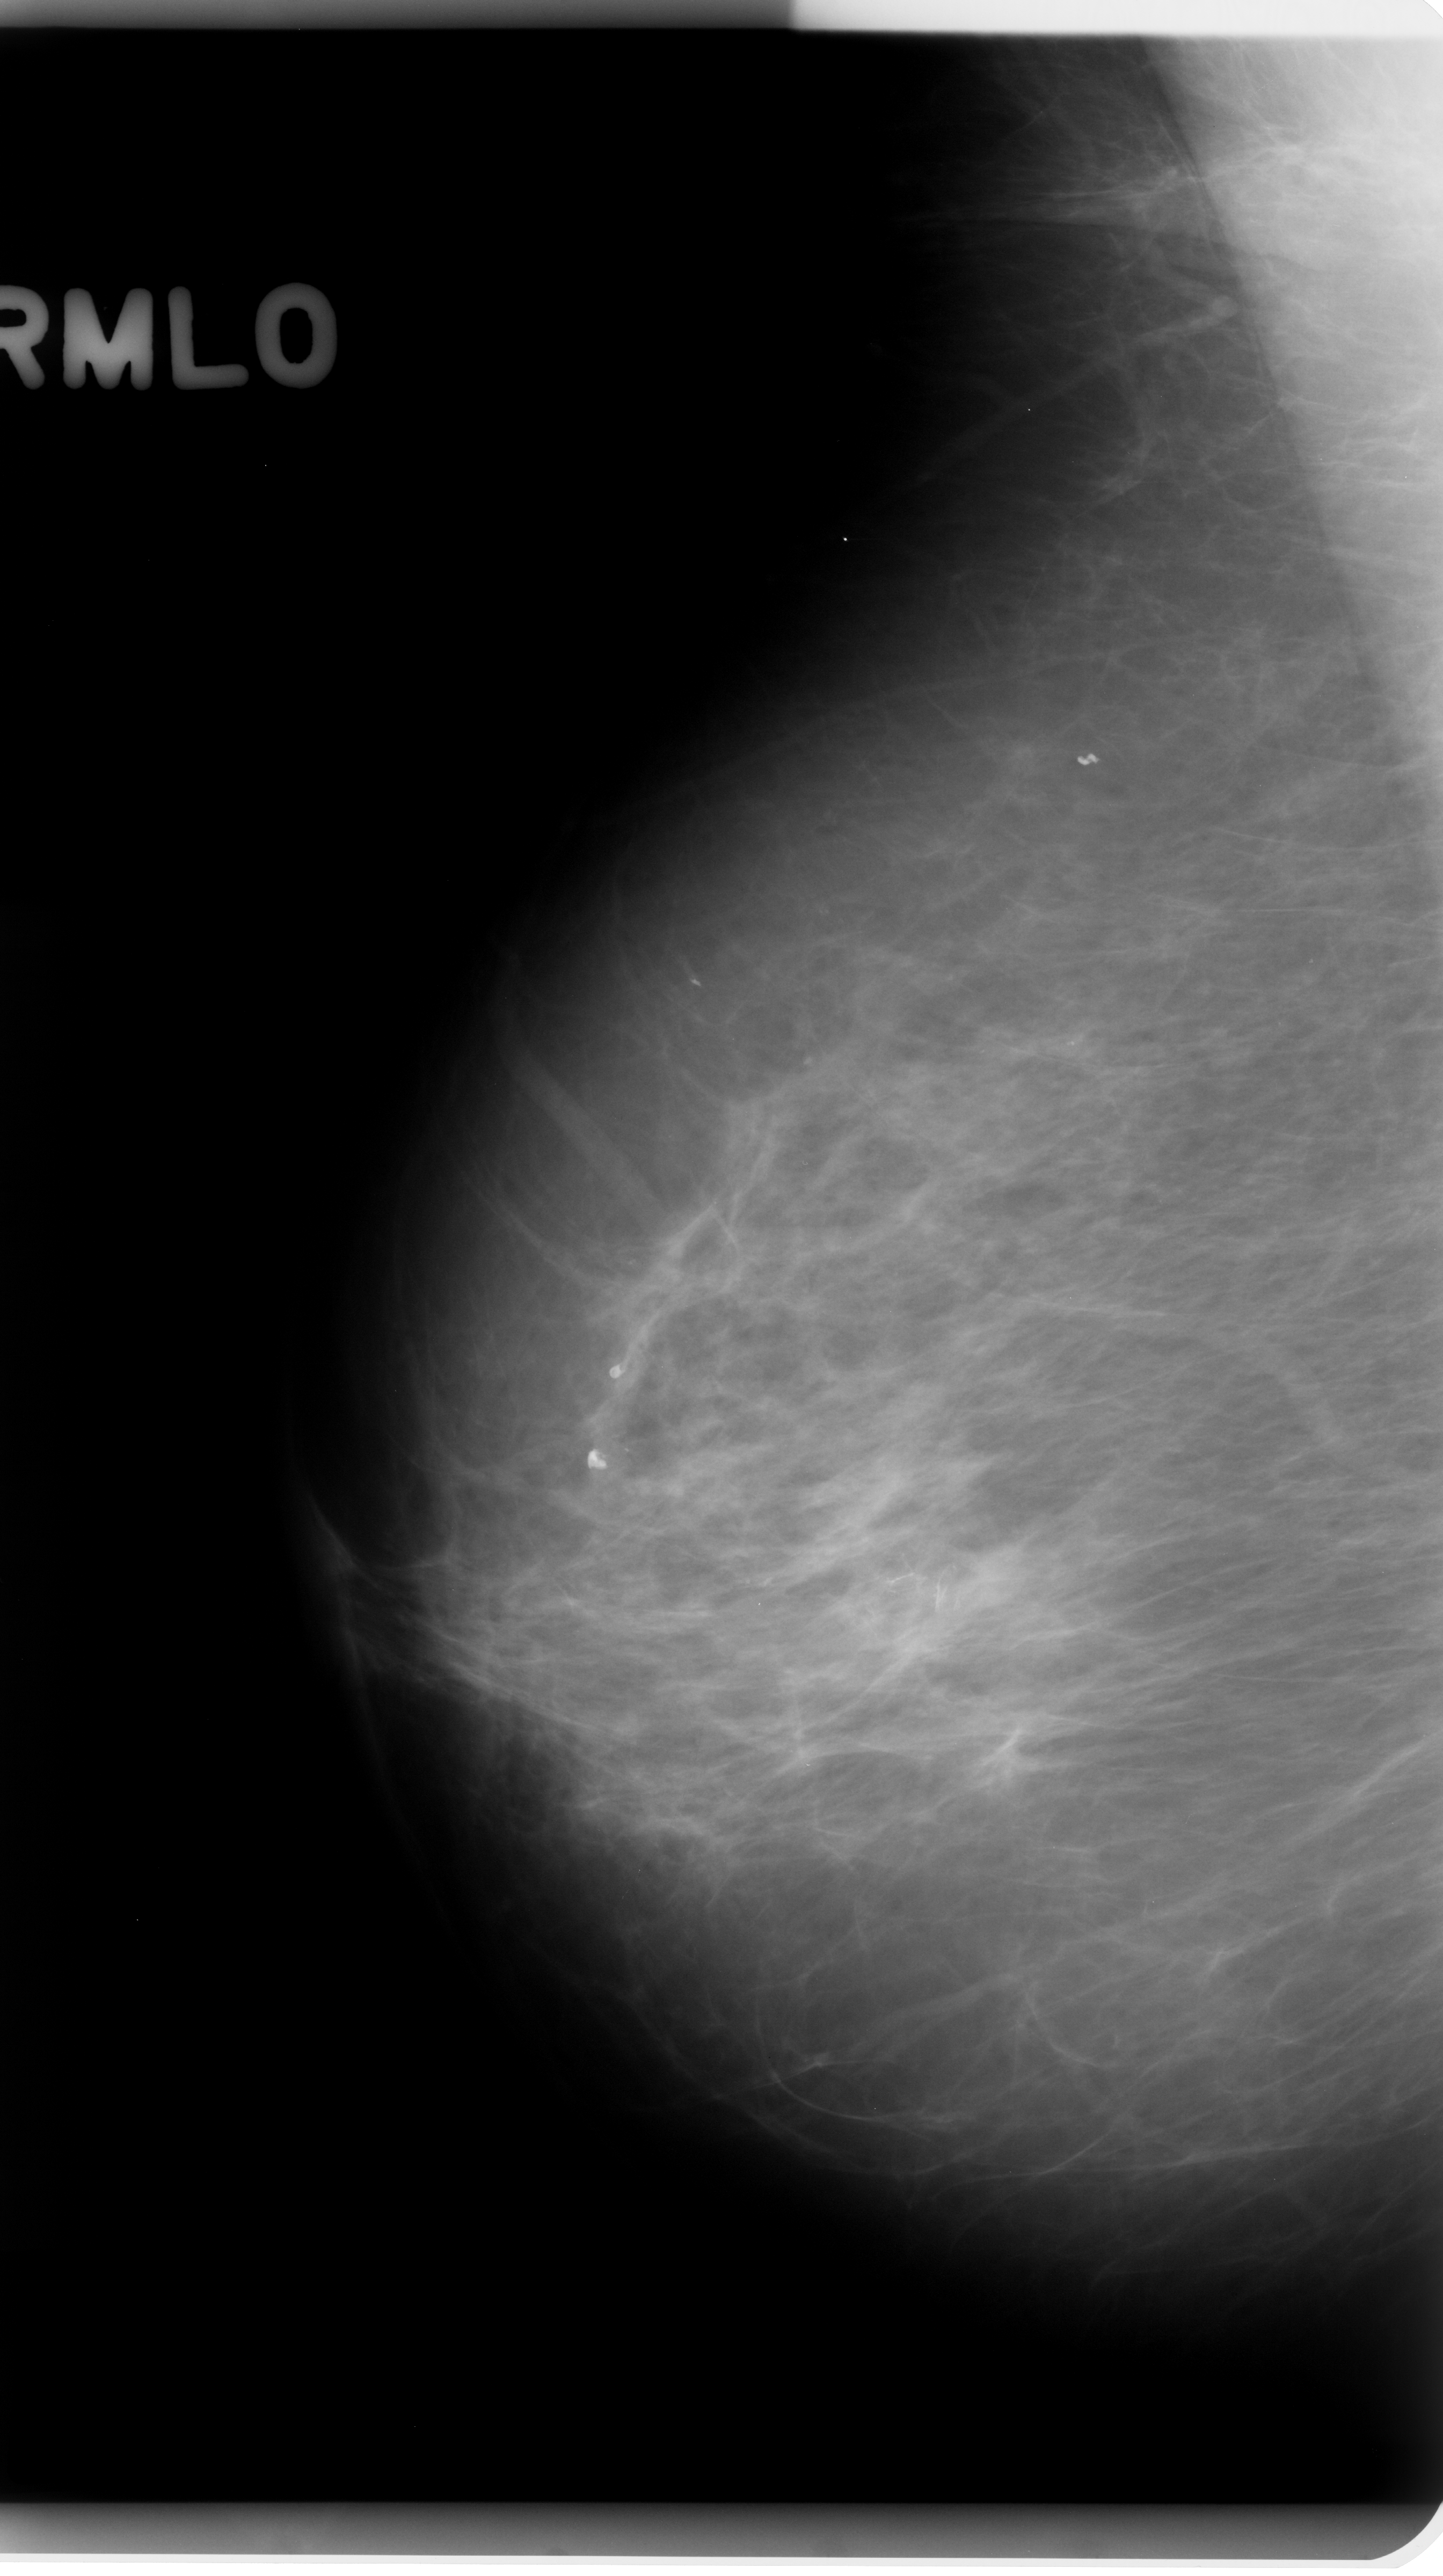
Digitized screen-film mammogram. Right breast. Mediolateral oblique (MLO) view. Breast composition: scattered fibroglandular densities (BI-RADS density category 2 of 4). 1443 × 2576 image matrix.
Expert-marked regions of interest on this image (one box per marked abnormality):
- calcifications, morphology fine linear branching, distribution clustered; BI-RADS assessment category 4; pathology result (as recorded, not read from the image): benign: bounding box (x1, y1, x2, y2) in pixels: (815, 1433, 1019, 1671)